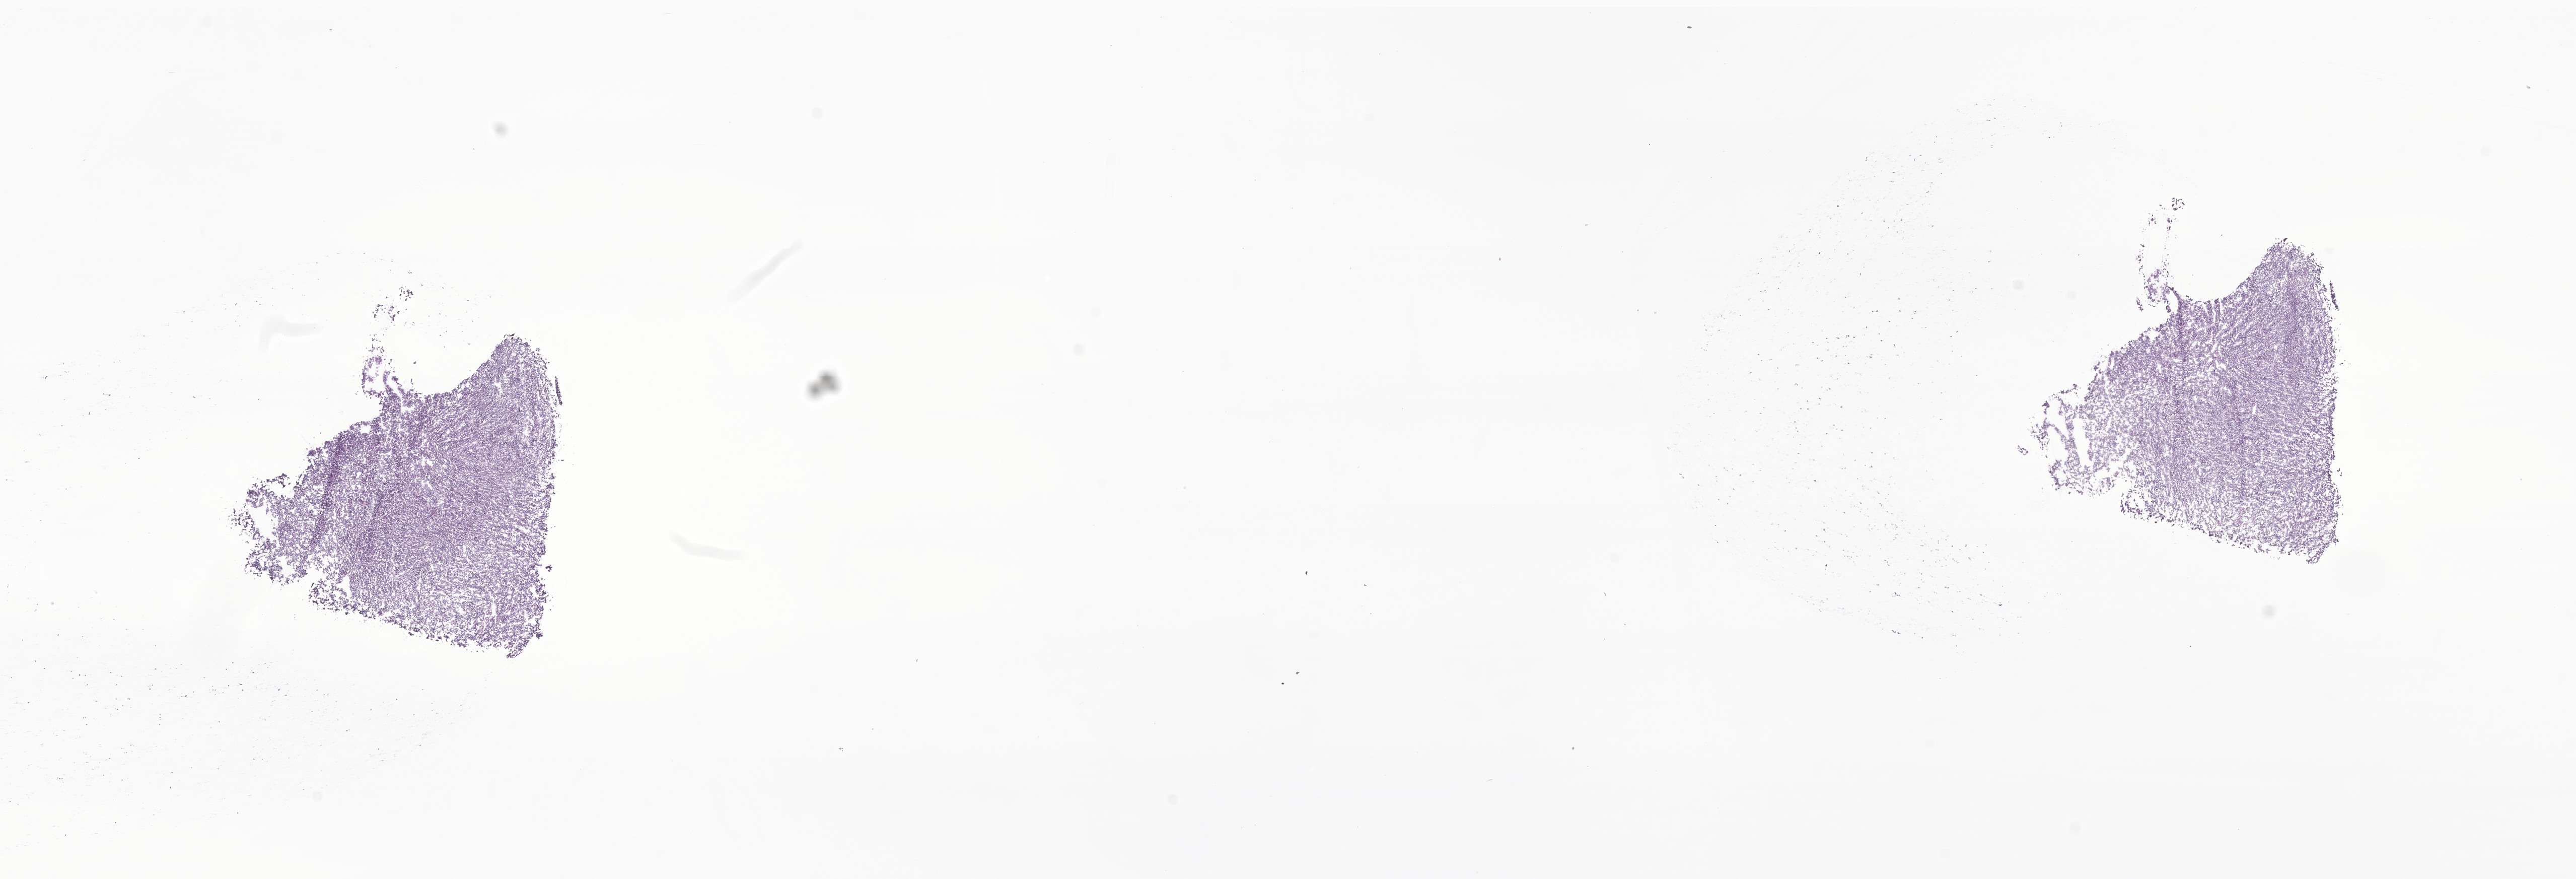
H&E whole-slide image of tumor tissue from the brain — whole scanned area (about 21.6 x 7.4 mm) shown as a low-resolution overview; cryosection (OCT / tissue freezing medium). Male patient, age 82 months (6 years 10 months).
Recorded diagnosis: Medulloblastoma, NOS.